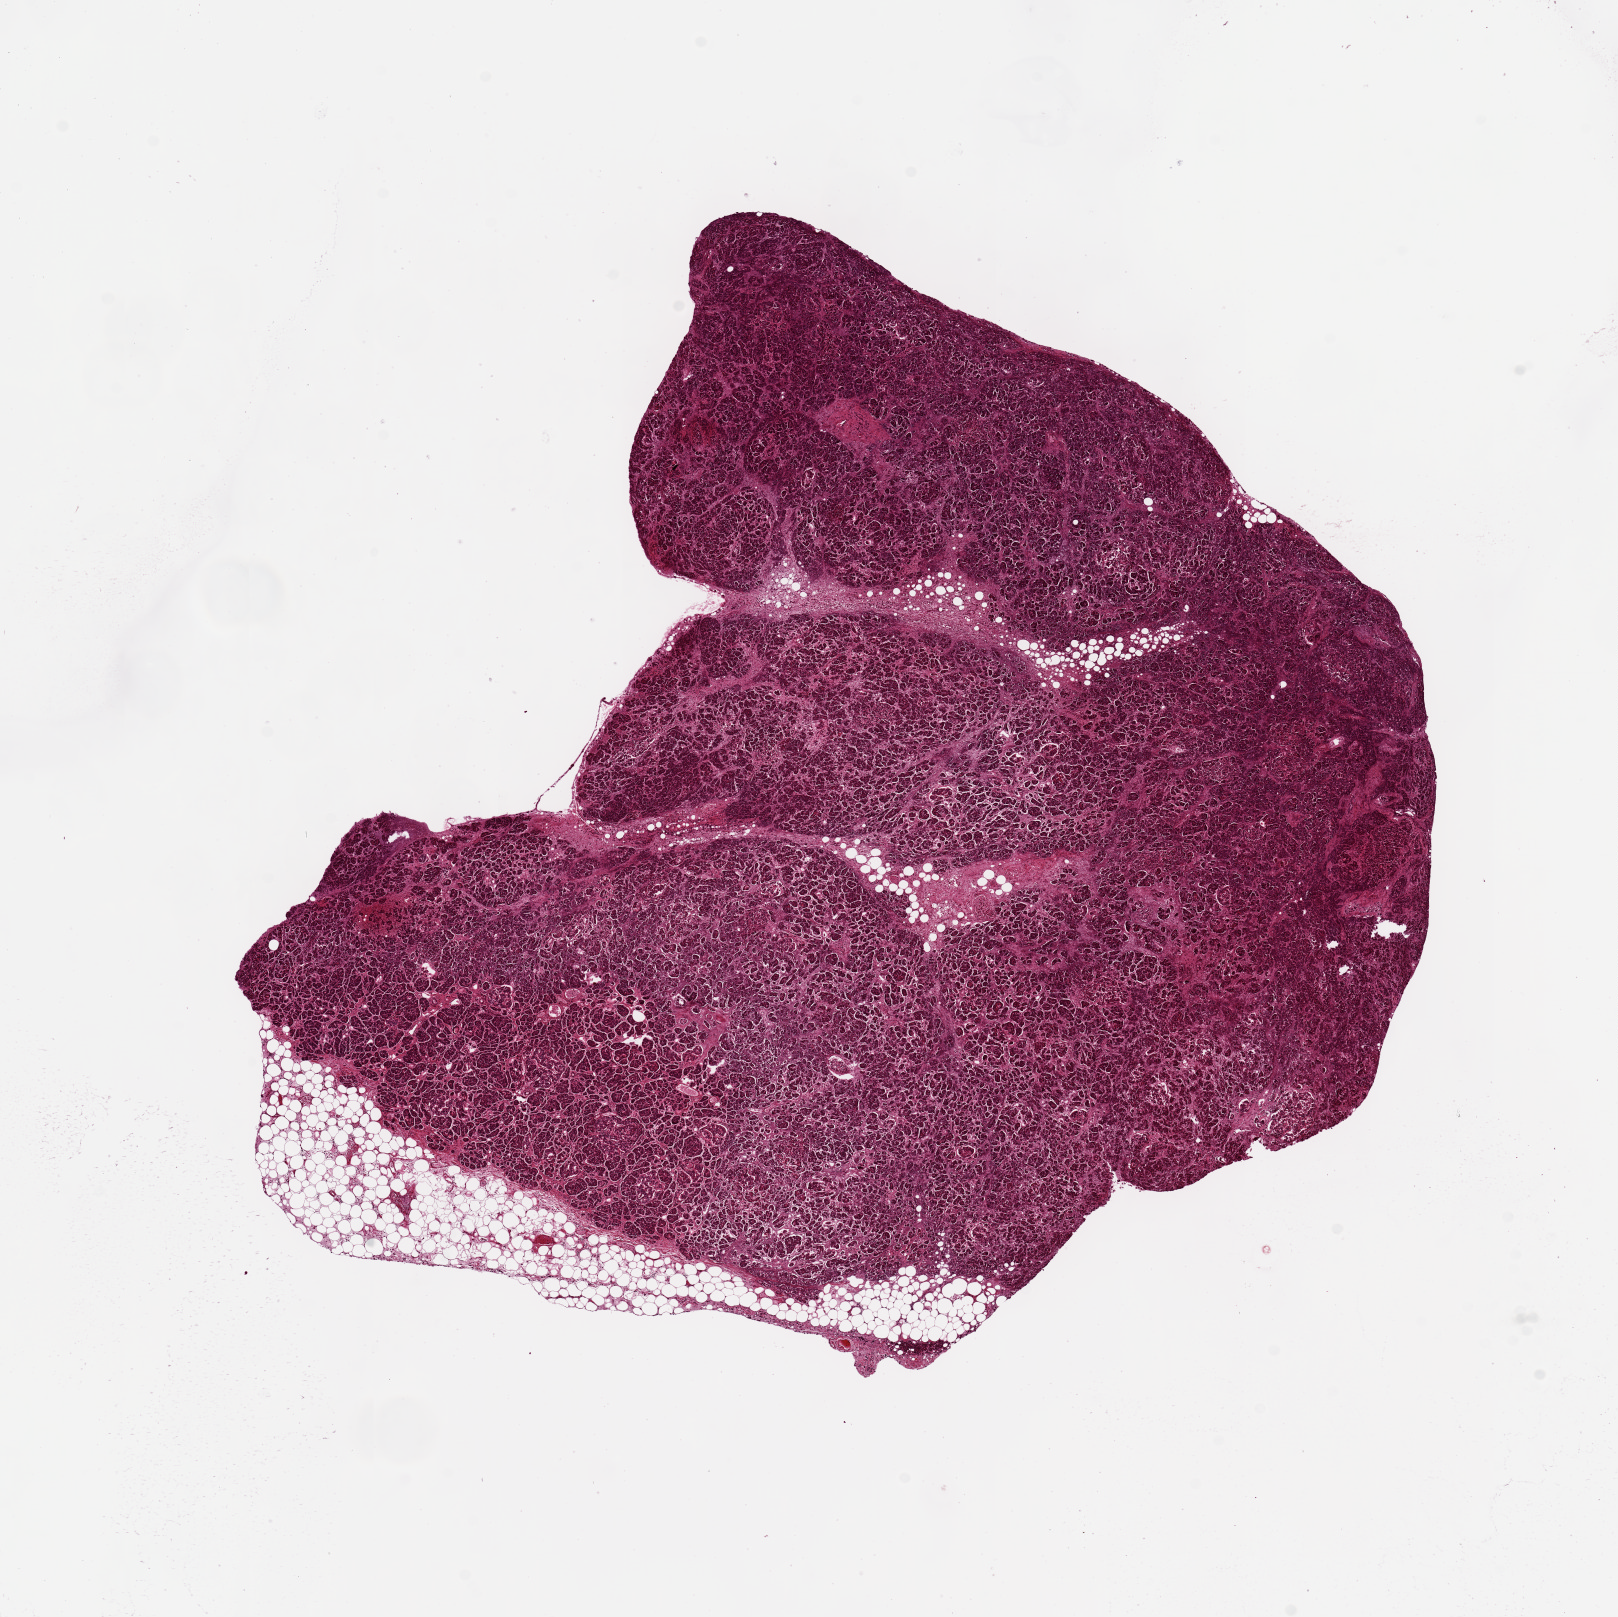
Whole-slide image, haematoxylin and eosin stain, shown as a low-resolution overview of the whole scanned area (about 12.8 x 12.8 mm). PAXgene-fixed paraffin-embedded (PFPE) section. Target tissue: pancreas. Tissue donor sample. Donor: male.
Pathologist's review note for this sample: 8.3x6.3mm. Peripancreatic fat shows moderate saponification.